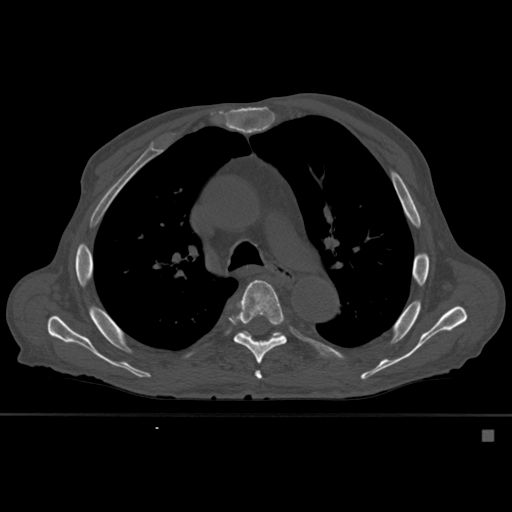
CT including the spine, one axial slice; bone window (W 1800 / L 400 HU); 512 × 512 image matrix, field of view 373 × 373 mm. Male patient, age 78 years. Case-level facts recorded for this patient, not image findings: primary cancer: prostate.
Outlined on this slice (semi-automatic segmentation, software-assisted and operator-edited):
- T5 vertebra: bounding box <255,371,262,380> (left, top, right, bottom; pixels)
- T6 vertebra: <228,280,287,364>
- T7 vertebra: <241,331,282,338>